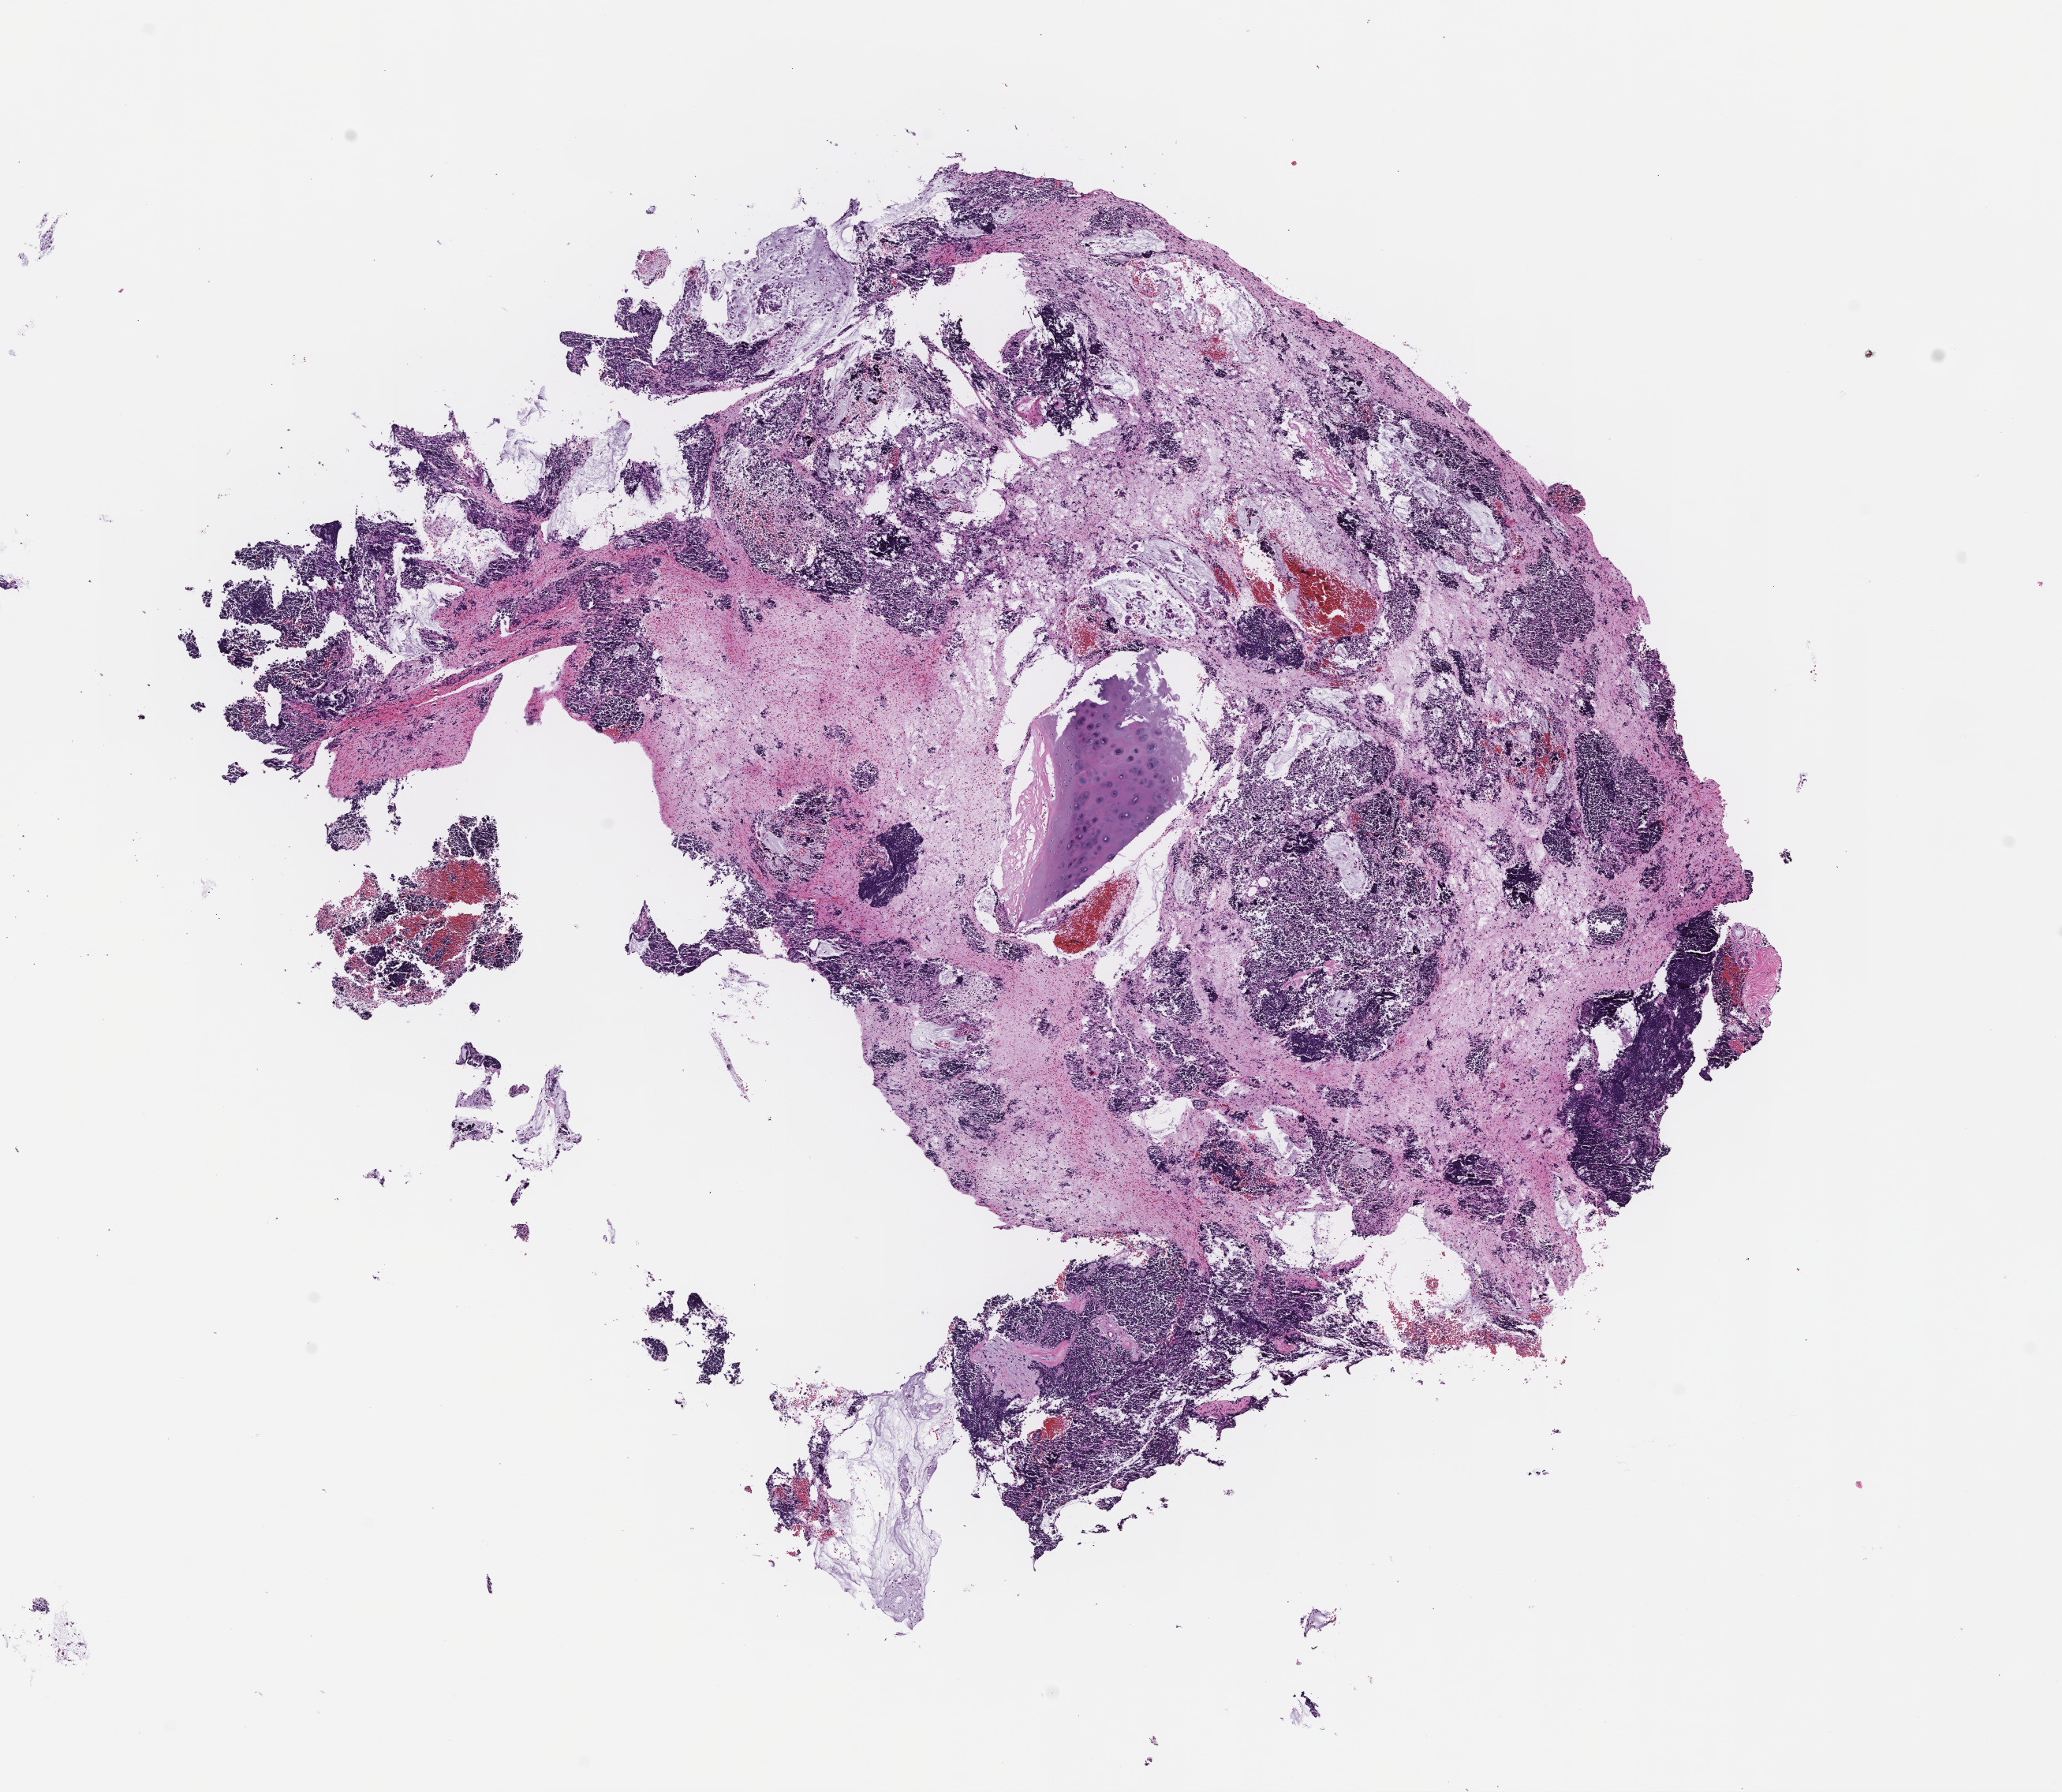
Whole-slide image, haematoxylin and eosin stain, a low-resolution overview of the entire scanned area, about 10.6 x 9.2 mm. Formalin-fixed, paraffin-embedded (FFPE) tissue. Archival tissue. Patient: male.
This section: metastasis (sampled organ not recorded). Primary diagnosis of the patient: Small Cell Lung Carcinoma.